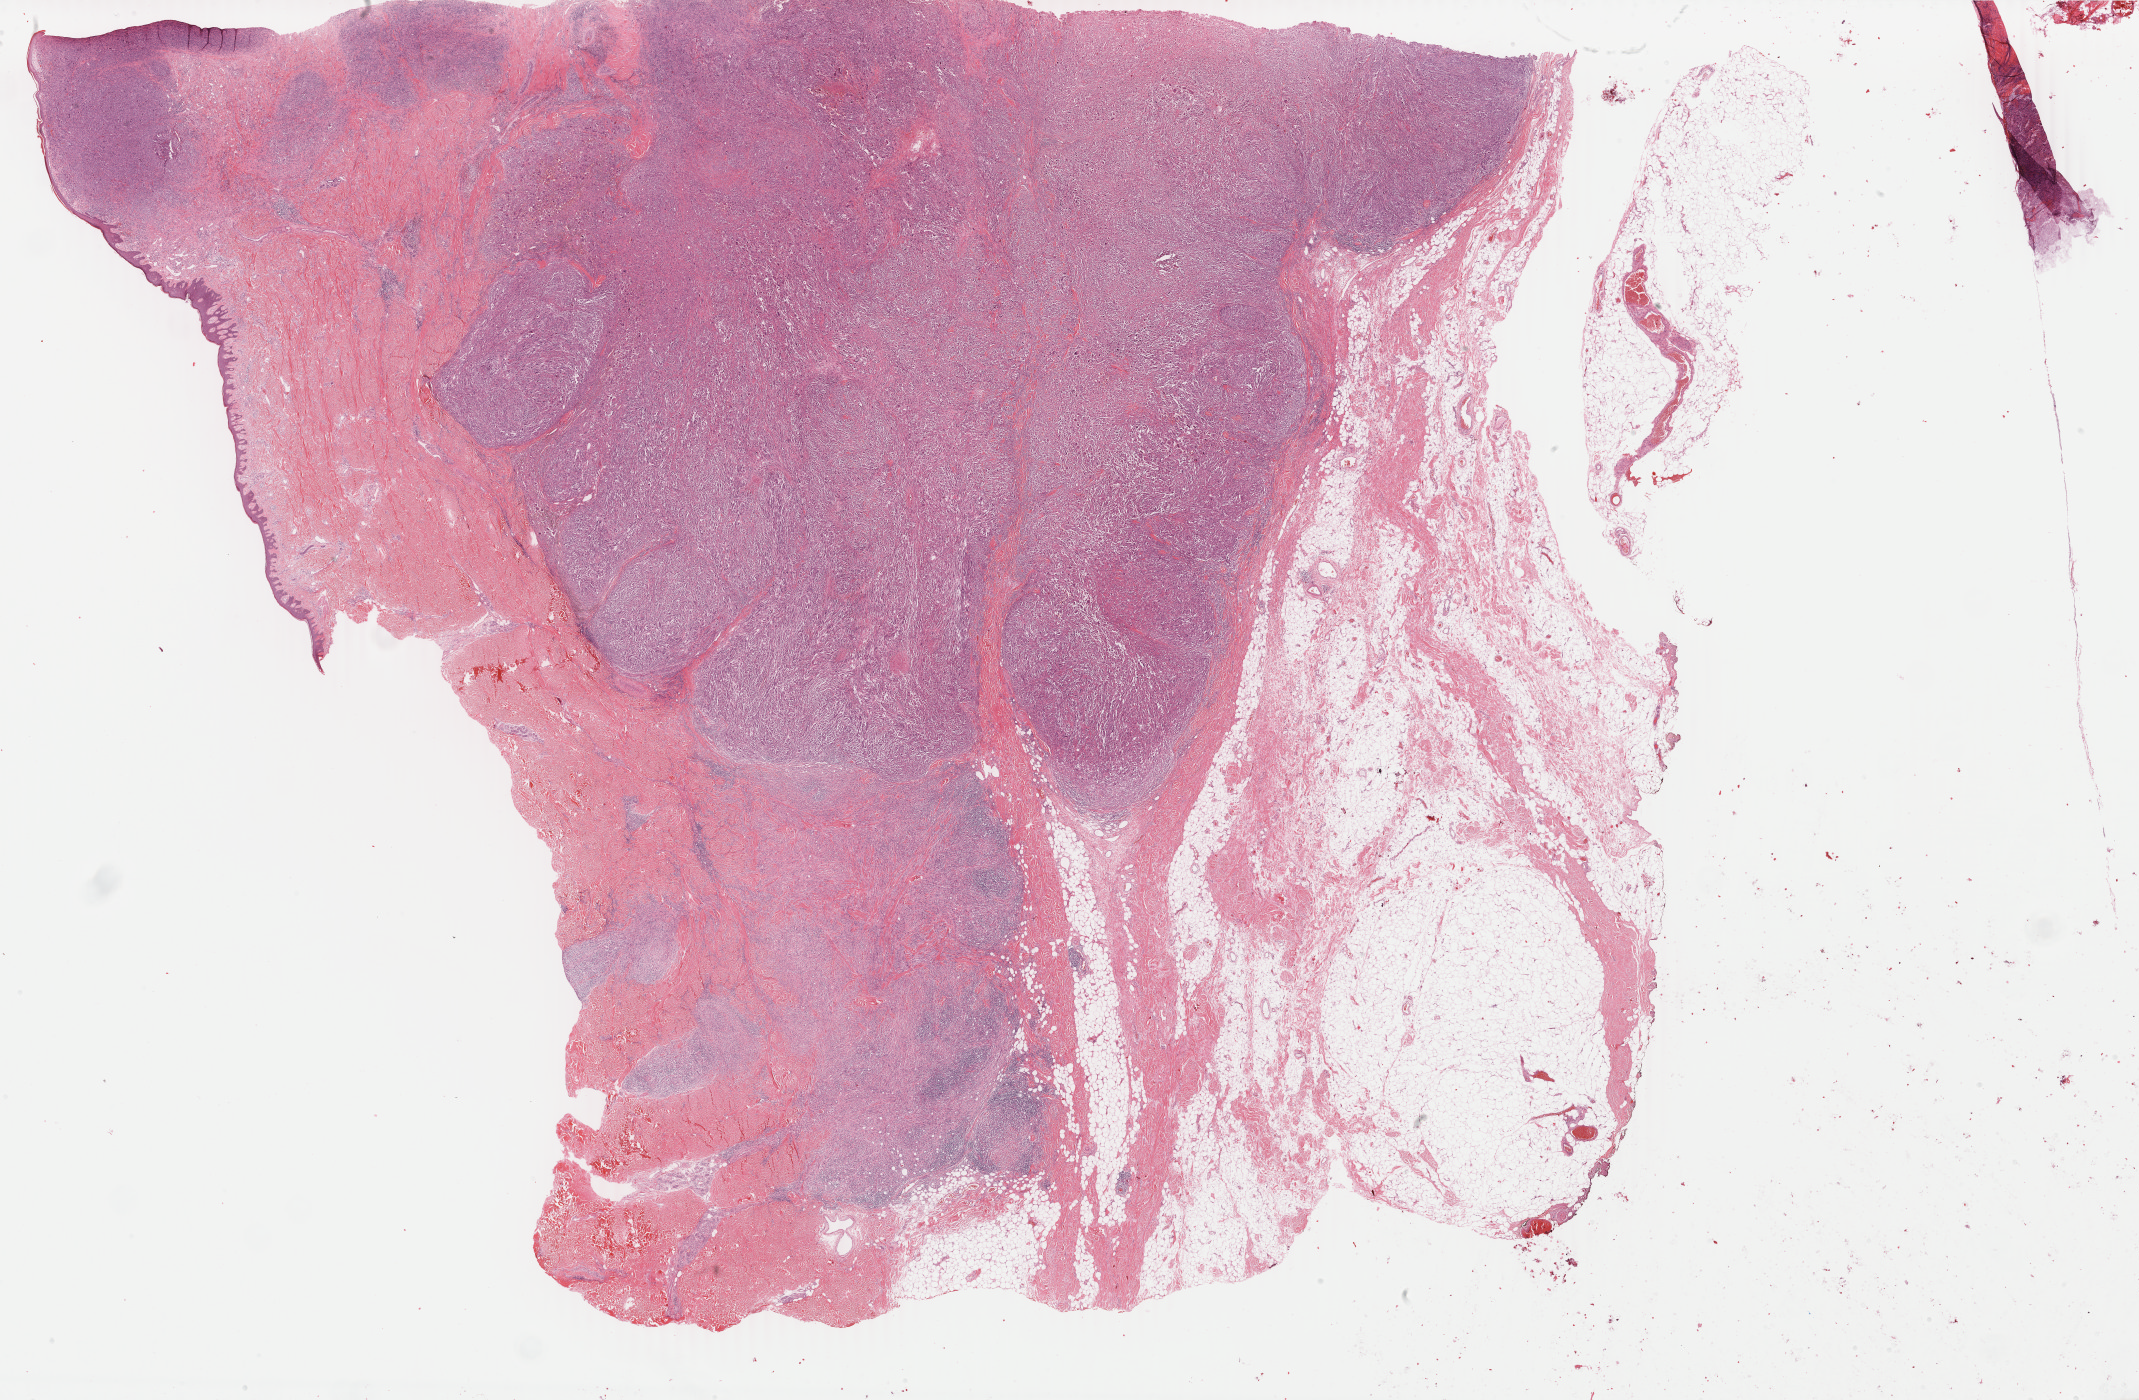
H&E-stained whole-slide image, whole scanned area (about 34.0 x 22.3 mm) shown as a low-resolution overview; formalin-fixed paraffin-embedded (FFPE) diagnostic section; sample: primary tumour, skin. Patient: male, age at initial diagnosis 79 years.
Diagnosis: Malignant melanoma, NOS.